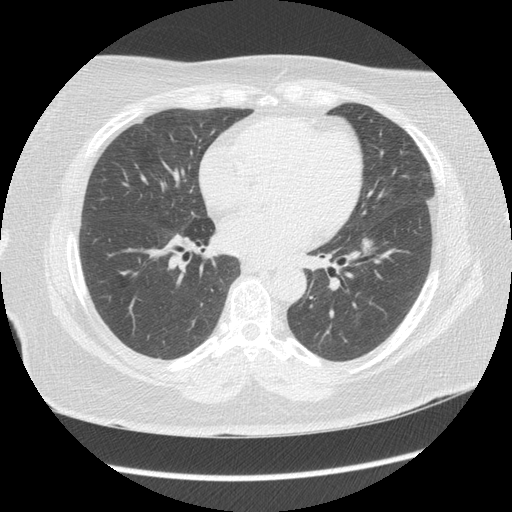
Low-dose screening chest CT, one axial slice. Slice 64 of 144 in the series (ordered by position). Lung window (W 1500 / L -600 HU). 2.5 mm slice thickness. 512 × 512 image matrix, field of view 360 × 360 mm.
Structures marked on this image (expert manual segmentation):
- lesion 1 (tumor, lower lobe of left lung): bounding box [x1, y1, x2, y2] px = [362, 237, 373, 253]